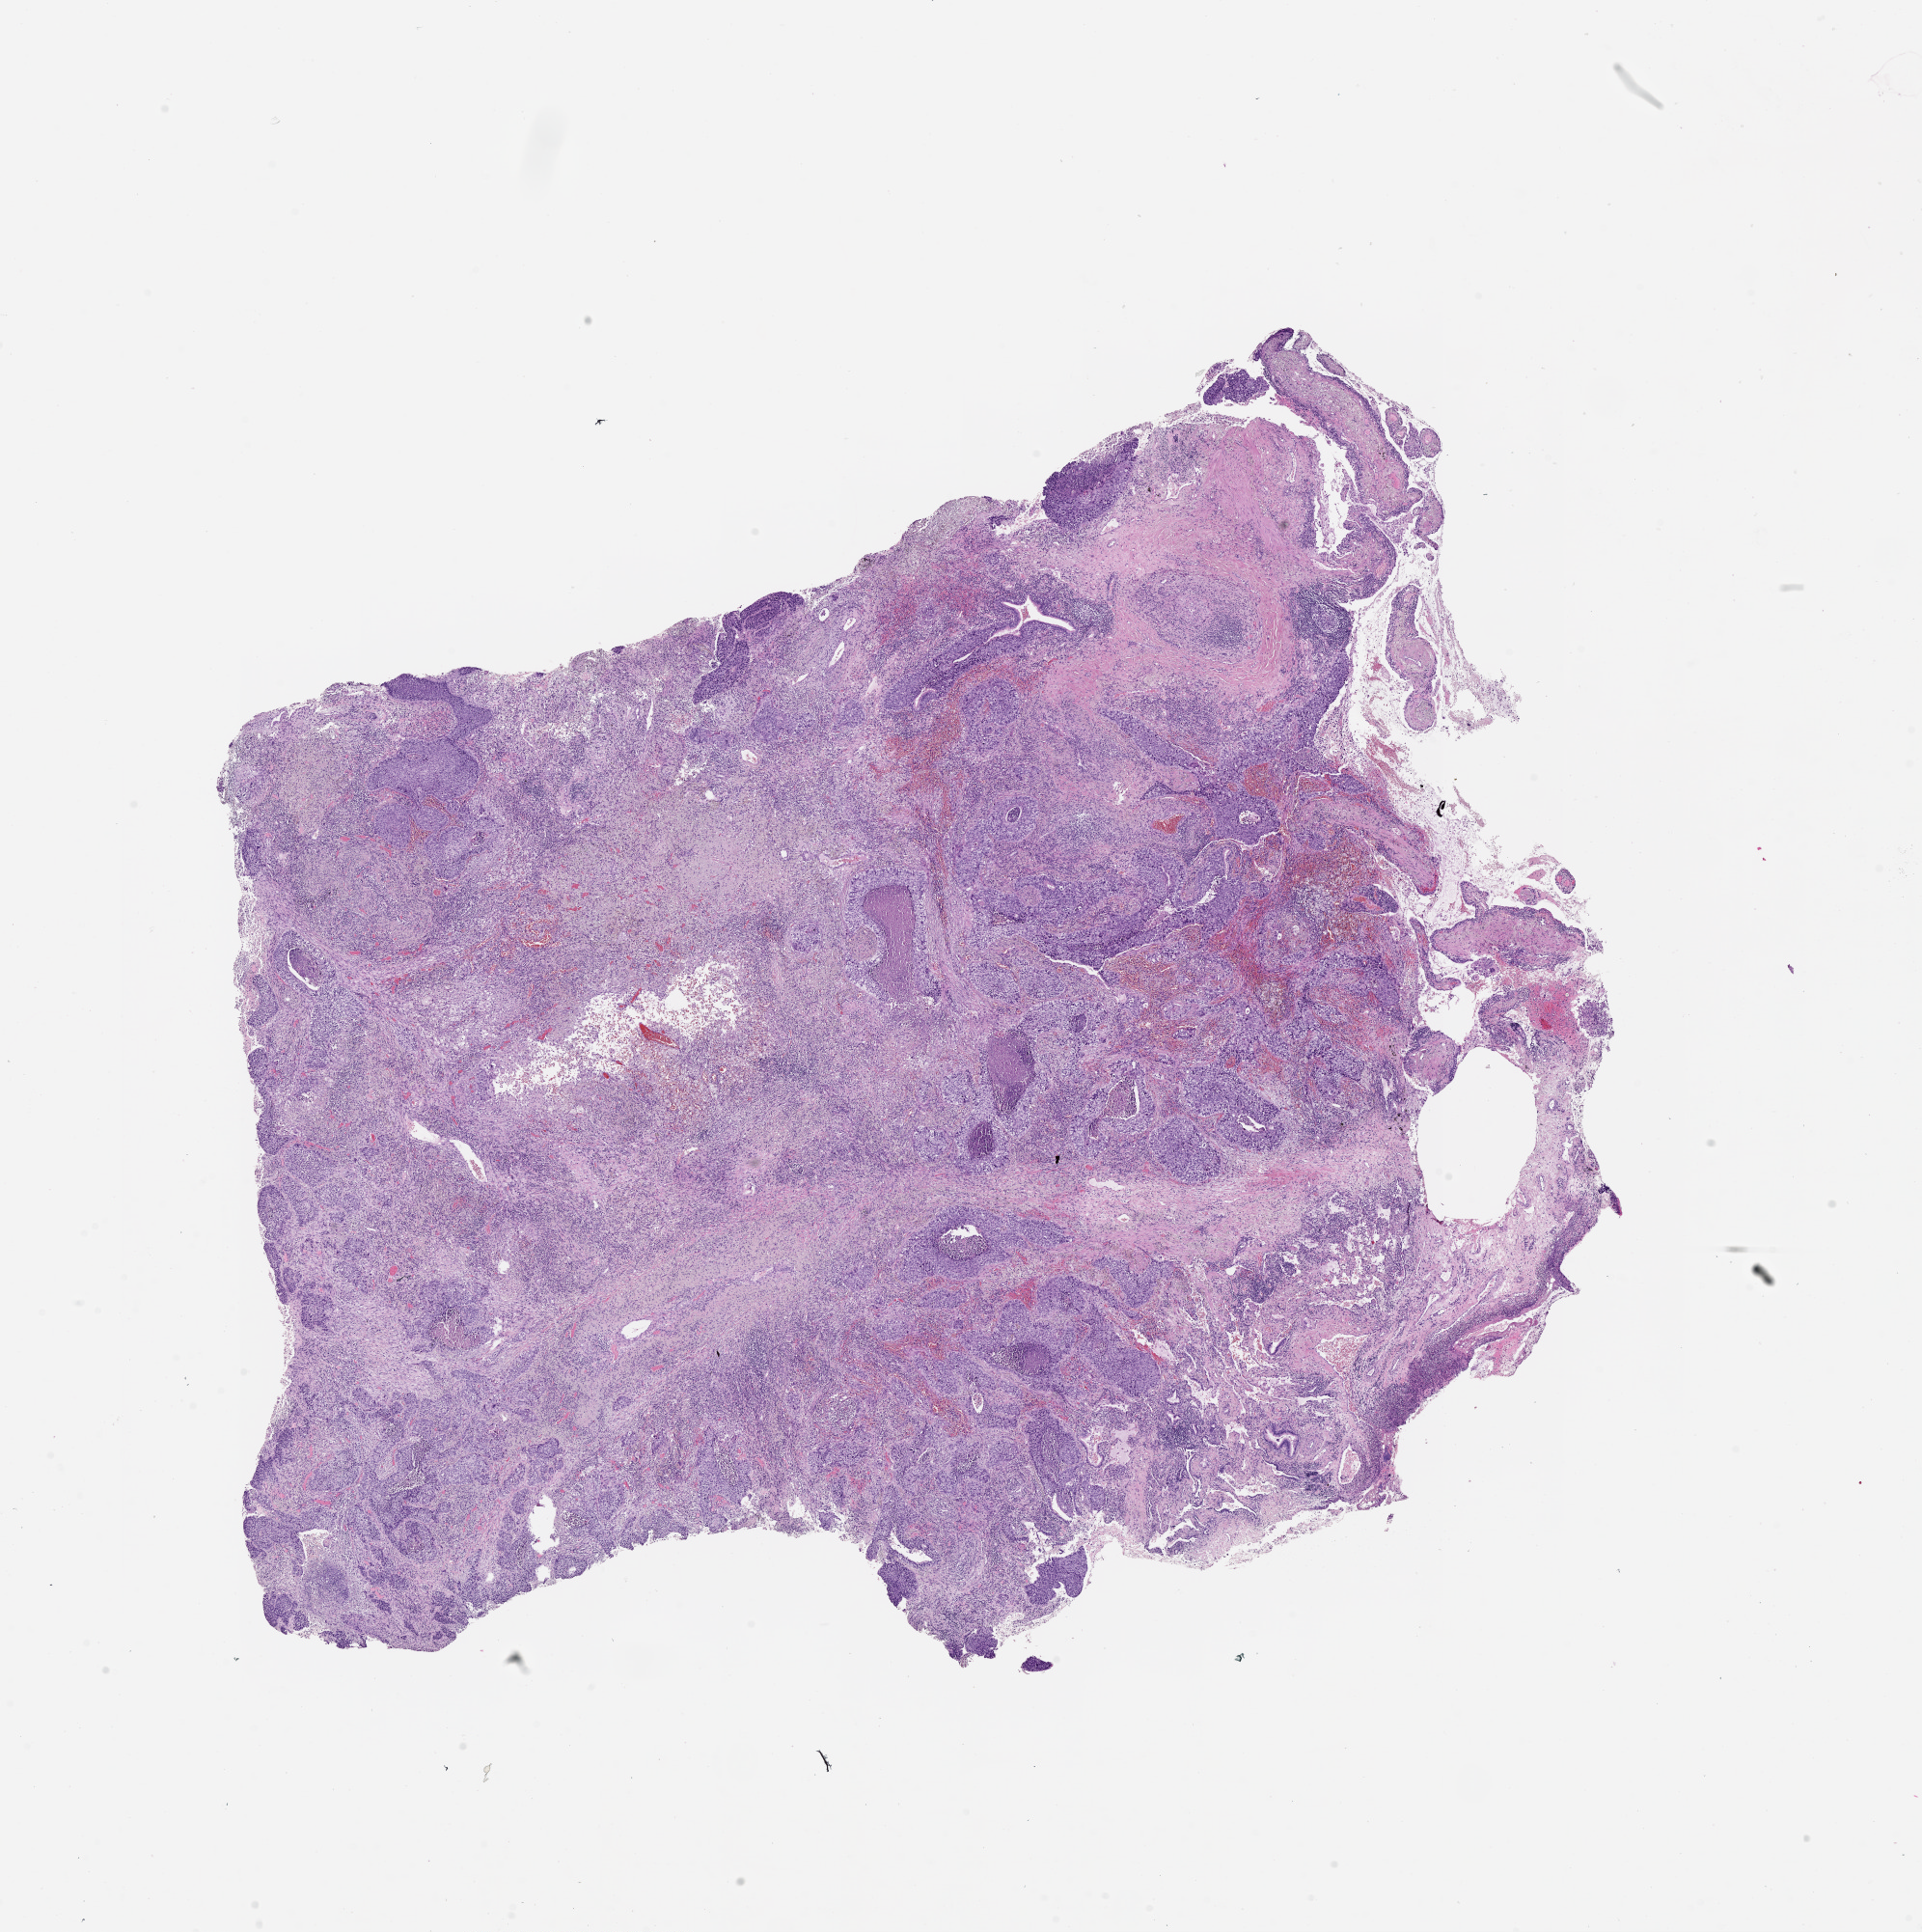
Whole-slide histology image, Hematoxylin and eosin (H&E) stained, low-resolution overview of the scanned area, about 16.0 x 16.1 mm (from a 20x scan); tumour tissue sample, lung. Male, 77 y/o.
* patient diagnosis (cohort enrolment): squamous cell carcinoma (lung)